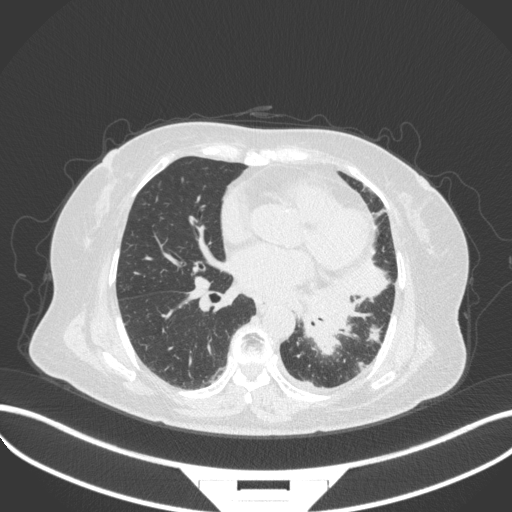
Chest CT, one axial slice. Position 160 of 328 along the scan axis. Lung window (W 1500 / L -600 HU). 1 mm slice thickness. 512 × 512 image matrix, field of view 400 × 400 mm. Female patient, age 69 years. Case-level facts recorded for this patient, not image findings: clinical TNM (as recorded): T2b N3 M1.
Outlined on this slice (rectangle marked by the reading radiologist):
- lung tumour (recorded histology: adenocarcinoma): bounding box [x1, y1, x2, y2] px = [297, 281, 363, 363]